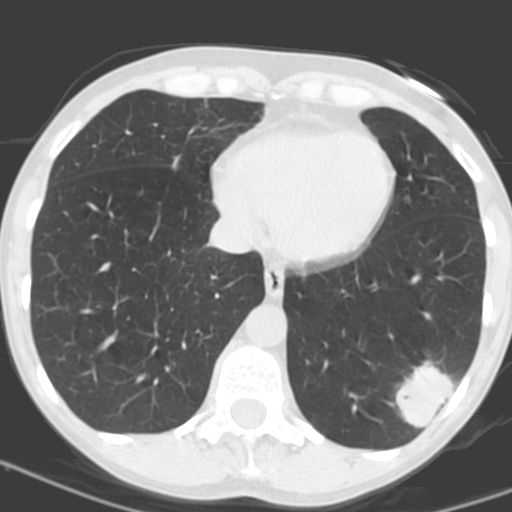
Low-dose screening chest CT, axial slice. First (baseline) screen. Lung window (W 1500 / L -600 HU). 3.2 mm slice thickness. Slice 108 of 156 in the series. 512 × 512 image matrix. Female, age 56 years at enrolment. Current smoker at enrolment.
Expert-annotated lung lesion, bounding box [x1, y1, x2, y2] px = [386, 359, 463, 428]. The exam's reader record, not a measurement of the box and not confirmed to be the same lesion: non-calcified nodule or mass ≥4 mm, left lower lobe, 31 × 23 mm, poorly defined margins, soft tissue attenuation, pre-existing on the prior screen: no. Participant outcome: lung cancer diagnosed 27 days after this screen — squamous cell carcinoma, NOS, left lower lobe, poorly differentiated (G3), stage IB (AJCC 6th edition), 35 mm at pathology.